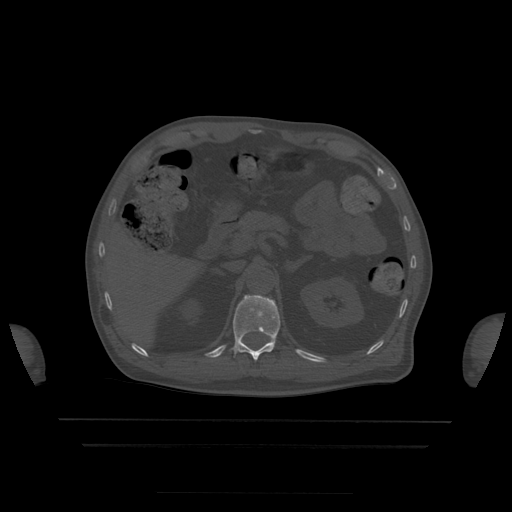
CT including the spine, one axial slice. Slice 194 of 522 in the series (ordered by position). Bone window (W 1800 / L 400 HU). 1.25 mm slice thickness. 512 × 512 image matrix, field of view 436 × 436 mm. Patient age 68 years. From the clinical record (not read from this slice): primary cancer: urothelial.
Structures marked on this image (semi-automatic segmentation, software-assisted and operator-edited):
- T12 vertebra: bounding box <232,295,281,361> (left, top, right, bottom; pixels)